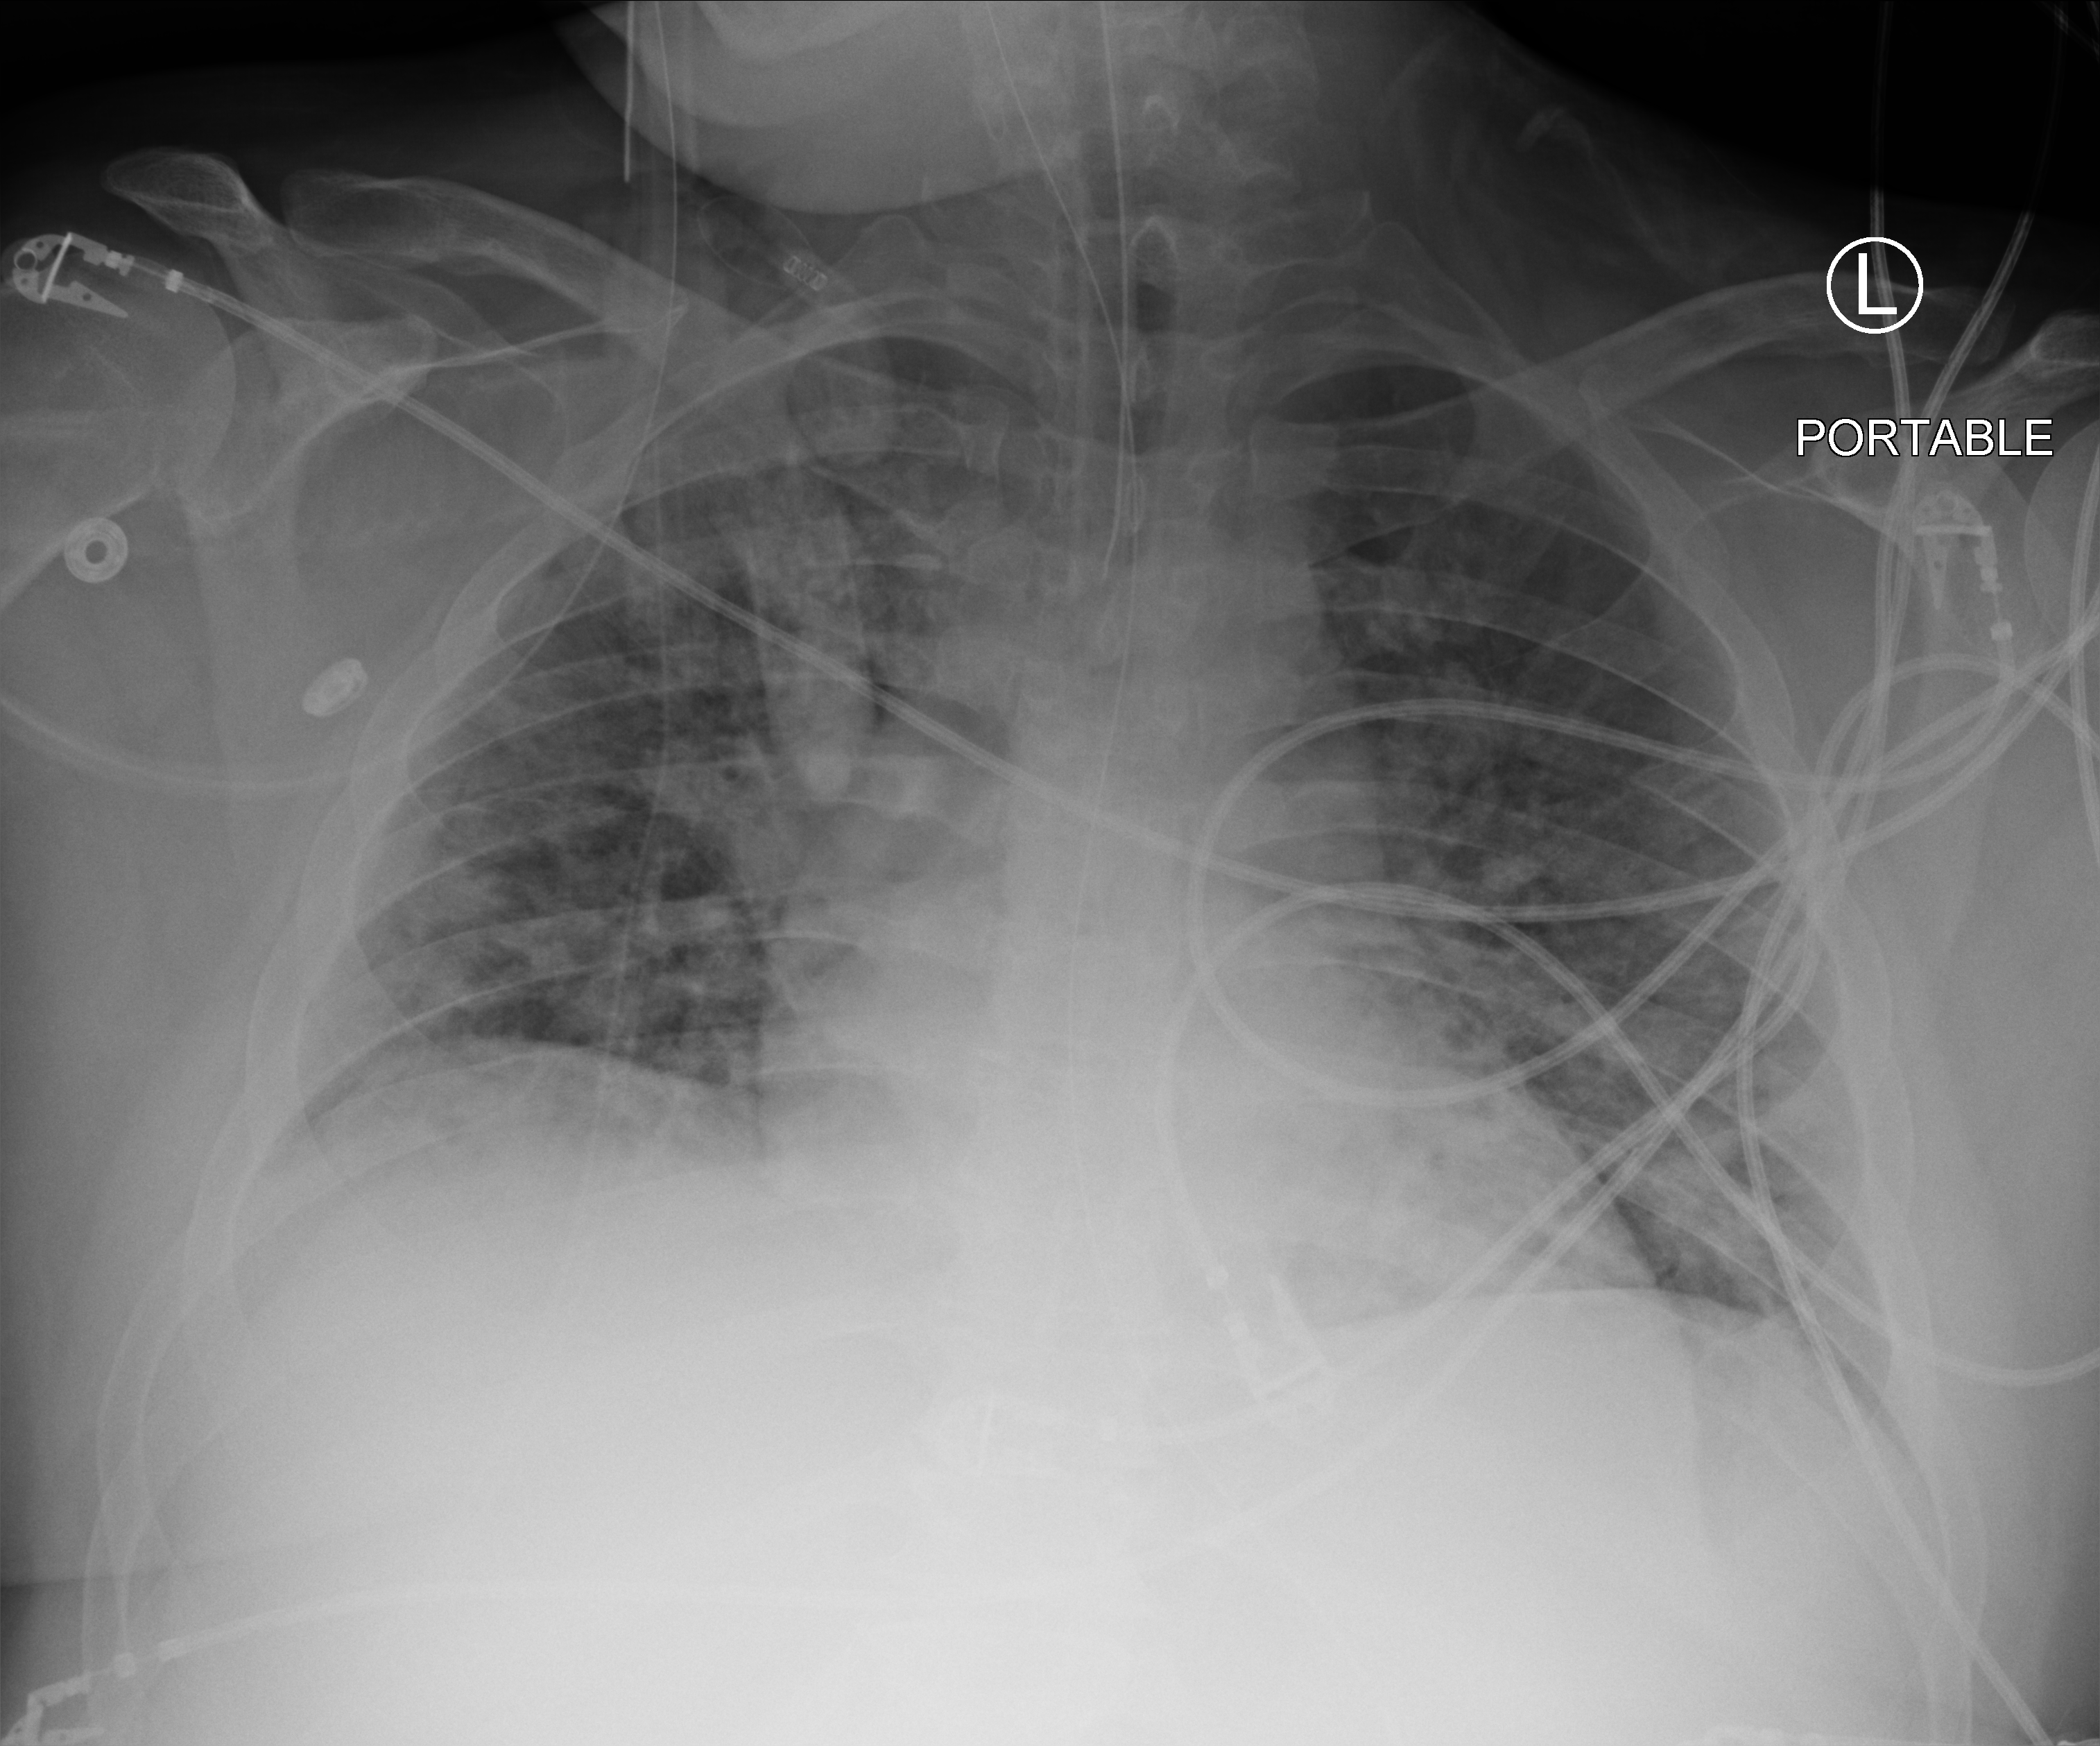
Portable chest radiograph, anteroposterior (AP) projection. Adult patient hospitalised with COVID-19, age 18–59 years.
Admission-level facts for this patient (not findings on this image; timing relative to this image not recorded):
- length of hospital stay: 31 days
- admitted to intensive care during this hospital stay: yes
- mechanically ventilated during this hospital stay: yes